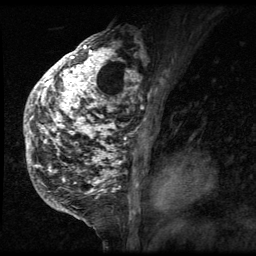
Breast MRI (dynamic contrast-enhanced), one sagittal slice; position 37 of 64 along the scan axis; 3 images stored at this slice position (order not interpretable as contrast timing); 1.5 T; TE 4.2 ms, TR 9 ms; 2.5 mm slice thickness; 256 × 256 image matrix, field of view 180 × 180 mm. Female patient, age 50 years. Case-level facts recorded for this patient, not image findings: setting: breast cancer imaged before/during neoadjuvant chemotherapy; receptor status: triple-negative.
Annotated regions visible in this slice (semi-automatically segmented with operator editing):
- analysis volume of interest (the breast-tissue region the enhancement analysis was run in; not a lesion): box from (x=24, y=39) to (x=140, y=212) px
- tumour enhancement mask (voxels above the 140 % enhancement threshold inside the analysis volume of interest): (x=24, y=39)–(x=140, y=212)